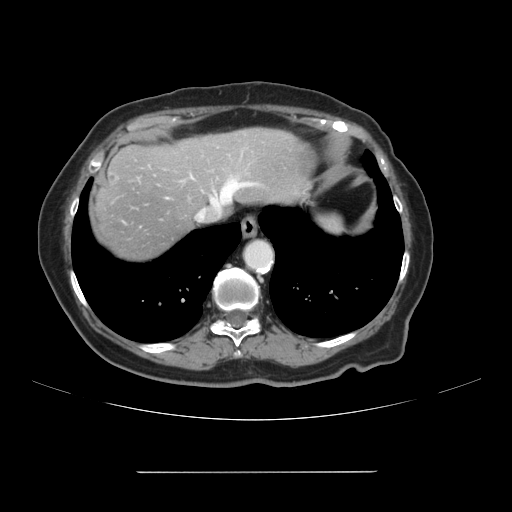
Contrast-enhanced abdominal CT, one axial slice. Slice 95 of 111 in the series (ordered by position). 120 kVp. Intravenous contrast given. Soft-tissue window (W 400 / L 40 HU). 512 × 512 image matrix, field of view 400 × 400 mm. Female patient, age 74 years. From the clinical record (not read from this slice): diagnosis: colorectal cancer liver metastases, imaged before liver resection; multiple liver metastases: yes; largest metastasis: 1.1 cm; chemotherapy before resection: yes.
Annotated regions visible in this slice (outlined manually by an expert reader):
- hepatic veins: bounding box <199,180,249,215> (left, top, right, bottom; pixels)
- liver: <92,128,311,263>
- planned liver remnant (the part of the liver to remain after resection): <181,128,311,211>
- portal vein (with intrahepatic branches): <216,197,218,199>
- liver metastasis: <108,174,116,182>